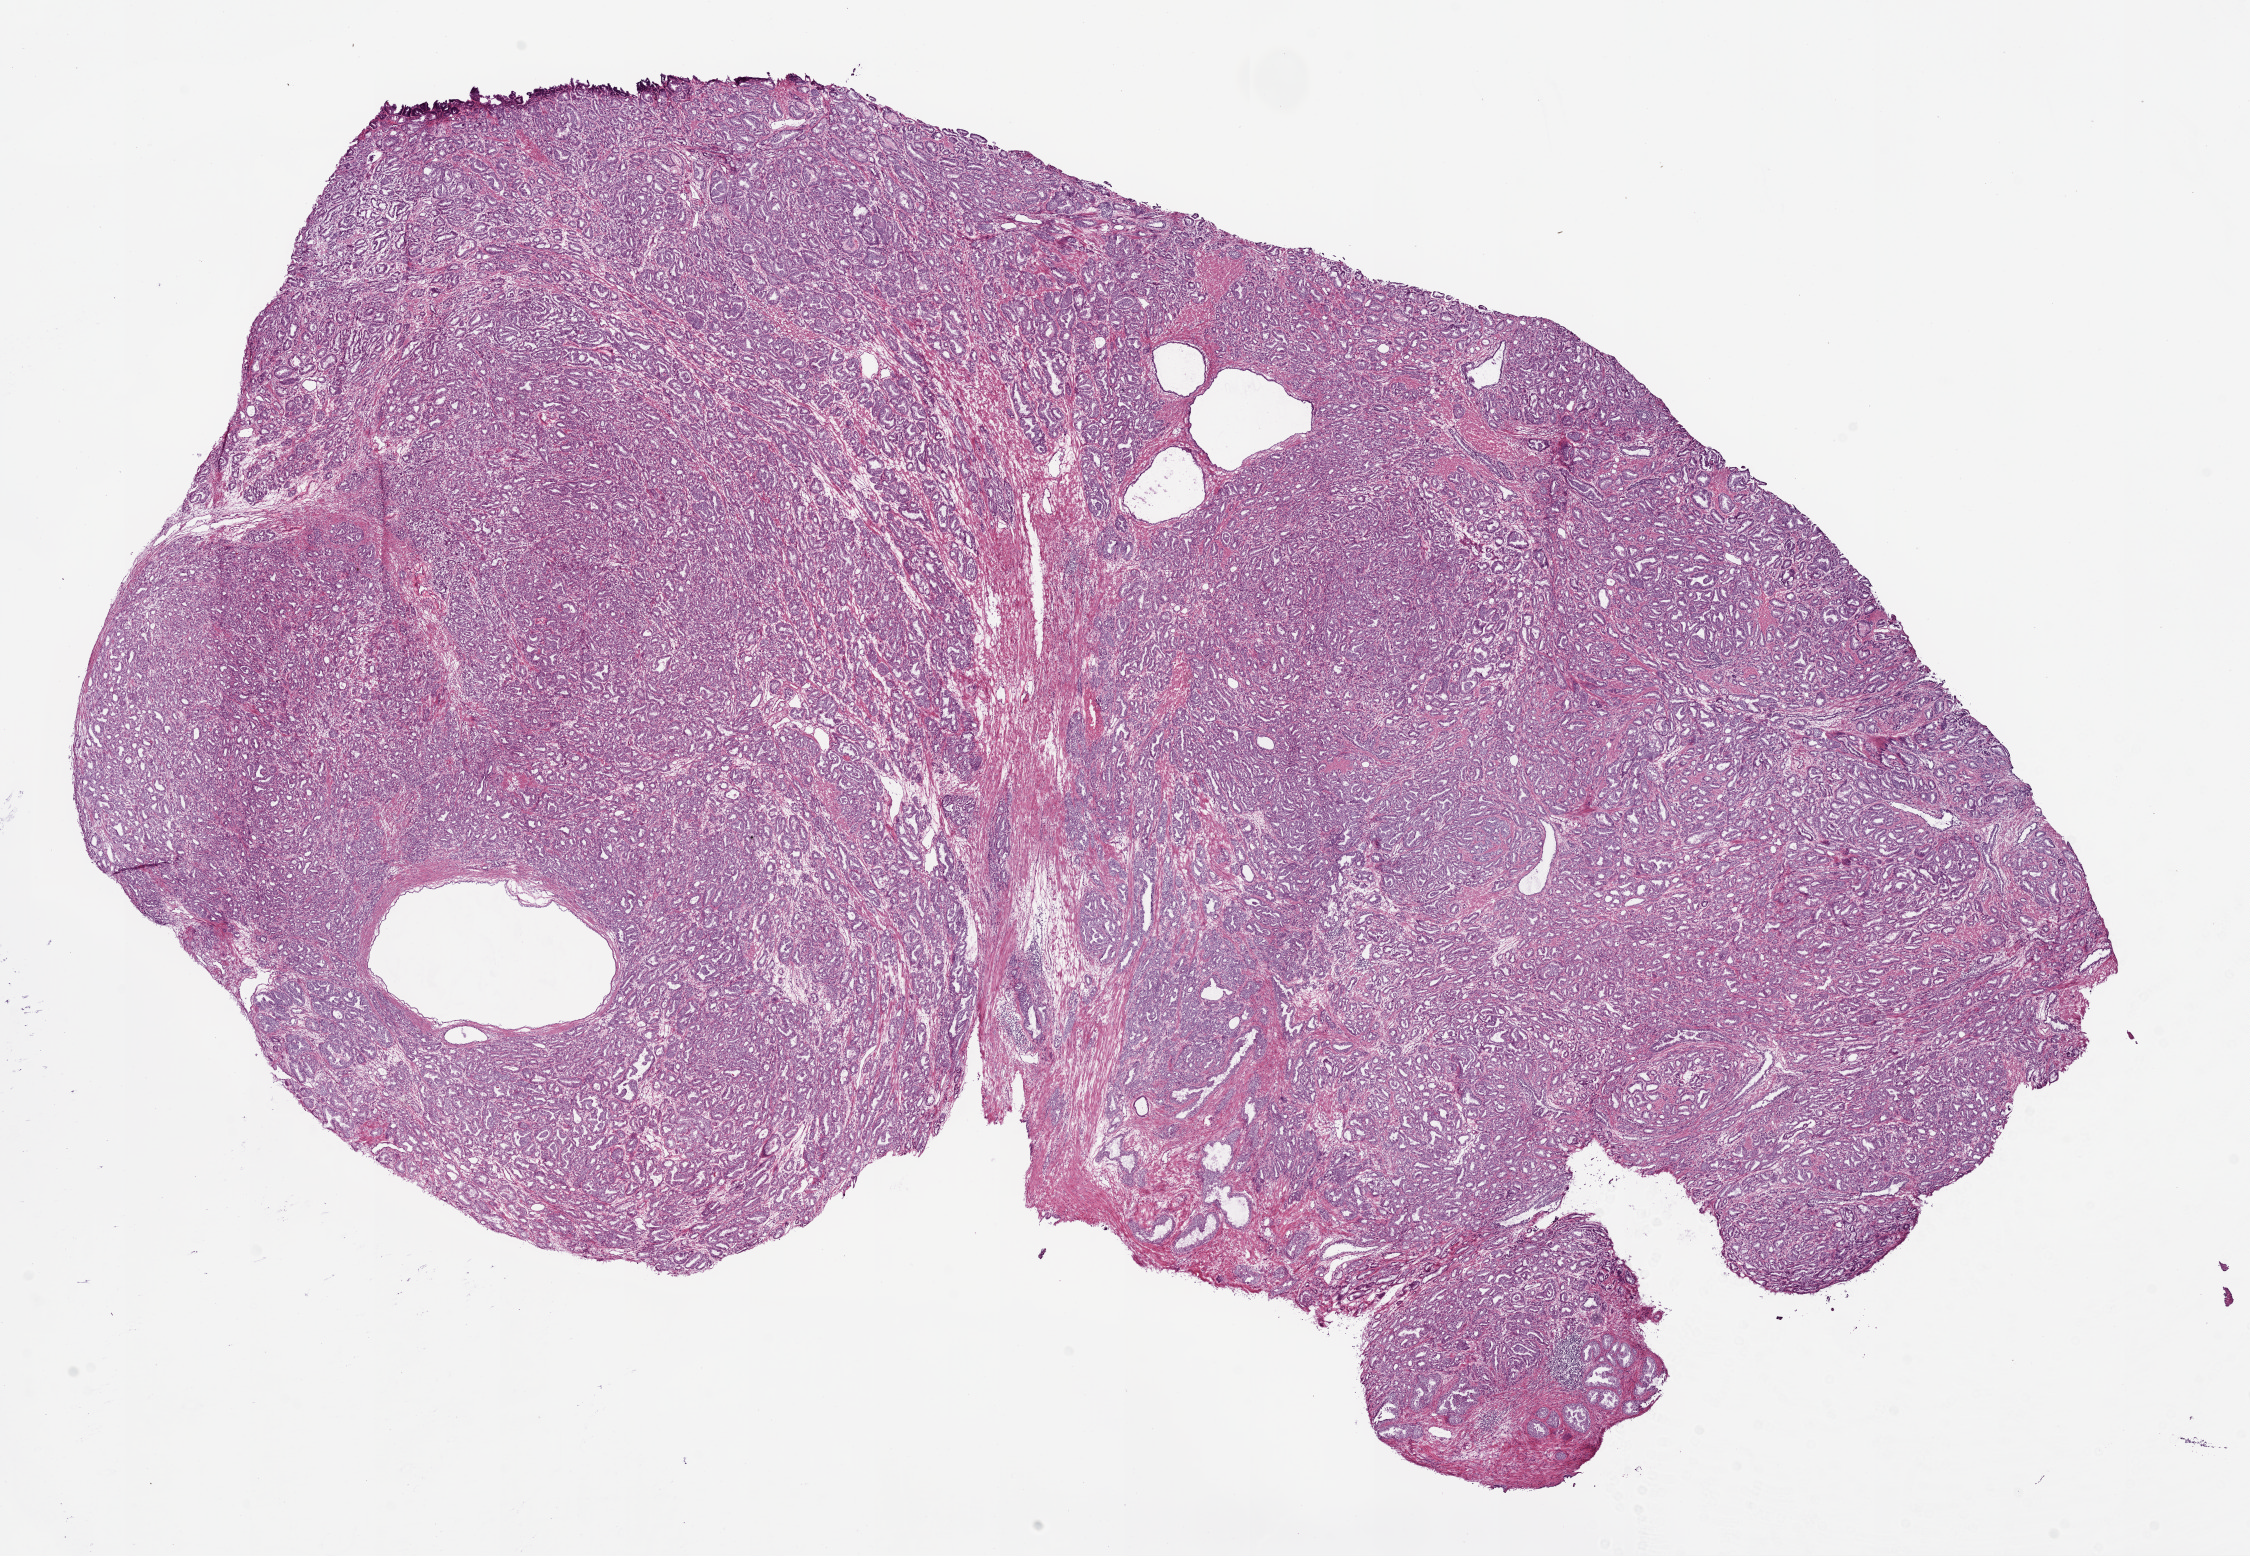
Whole-slide histology image, H&E — shown as a low-resolution overview of the whole scanned area (about 18.1 x 12.5 mm), frozen section from the top of the tissue portion, primary tumour sample from the prostate. Male patient; age at initial diagnosis 57 years. Gleason score: 7 (3+4). Slide review estimates, as recorded: tumour cells 75%, tumour nuclei 80%, normal cells 10%, stromal cells 15%, necrosis 0%. Infiltration values recorded for this section: lymphocyte infiltration 3%, monocyte infiltration 0%, neutrophil infiltration 0%.
• lymph nodes positive (case pathology): 0 of 8 examined
• pathologic diagnosis: Acinar cell carcinoma (prostate gland)